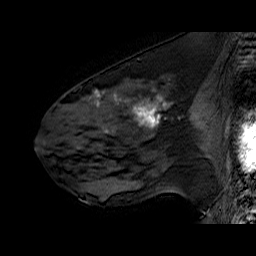
Breast MRI (dynamic contrast-enhanced), one sagittal slice; slice 29 of 60 in the series (ordered by position); dynamic contrast-enhanced series, time point 2 of 6 at this slice position (early post-contrast); 1.5 T; TE 6.4 ms, TR 32.9 ms; 256 × 256 image matrix, field of view 200 × 200 mm. Female patient. Case-level facts recorded for this patient, not image findings: setting: breast cancer imaged before/during neoadjuvant chemotherapy; receptor status: HER2-positive.
Annotated regions visible in this slice (semi-automatically segmented with operator editing):
- analysis volume of interest (the breast-tissue region the enhancement analysis was run in; not a lesion): bounding box [x1, y1, x2, y2] px = [51, 78, 196, 160]
- tumour enhancement mask (voxels above the 100 % enhancement threshold inside the analysis volume of interest): [94, 90, 167, 129]